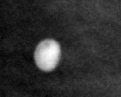
Region of interest cut from a scanned film mammogram (one marked finding); left breast; MLO view; BI-RADS breast density category 4 (scale 1–4).
- Calcifications, morphology round and regular / lucent center / punctate, distribution diffusely scattered; BI-RADS assessment category 2; subtlety rating 5 on a 1 (subtle) to 5 (obvious) scale; benign without callback (not worked up further).